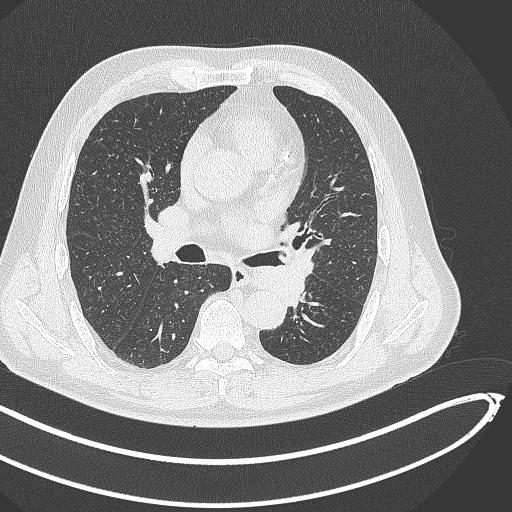
Chest CT, one axial slice; position 260 of 468 along the scan axis; reconstruction kernel B70f; lung window (W 1500 / L -600 HU); 1 mm slice thickness; 512 × 512 image matrix. Patient: male, 64 years. Case-level facts recorded for this patient, not image findings: clinical TNM (as recorded): T1c N0 M0; histopathological grade: G2.
Outlined on this slice (bounding box drawn by a radiologist):
- lung tumour (recorded histology: squamous cell carcinoma): bounding box [x1, y1, x2, y2] px = [247, 257, 317, 309]